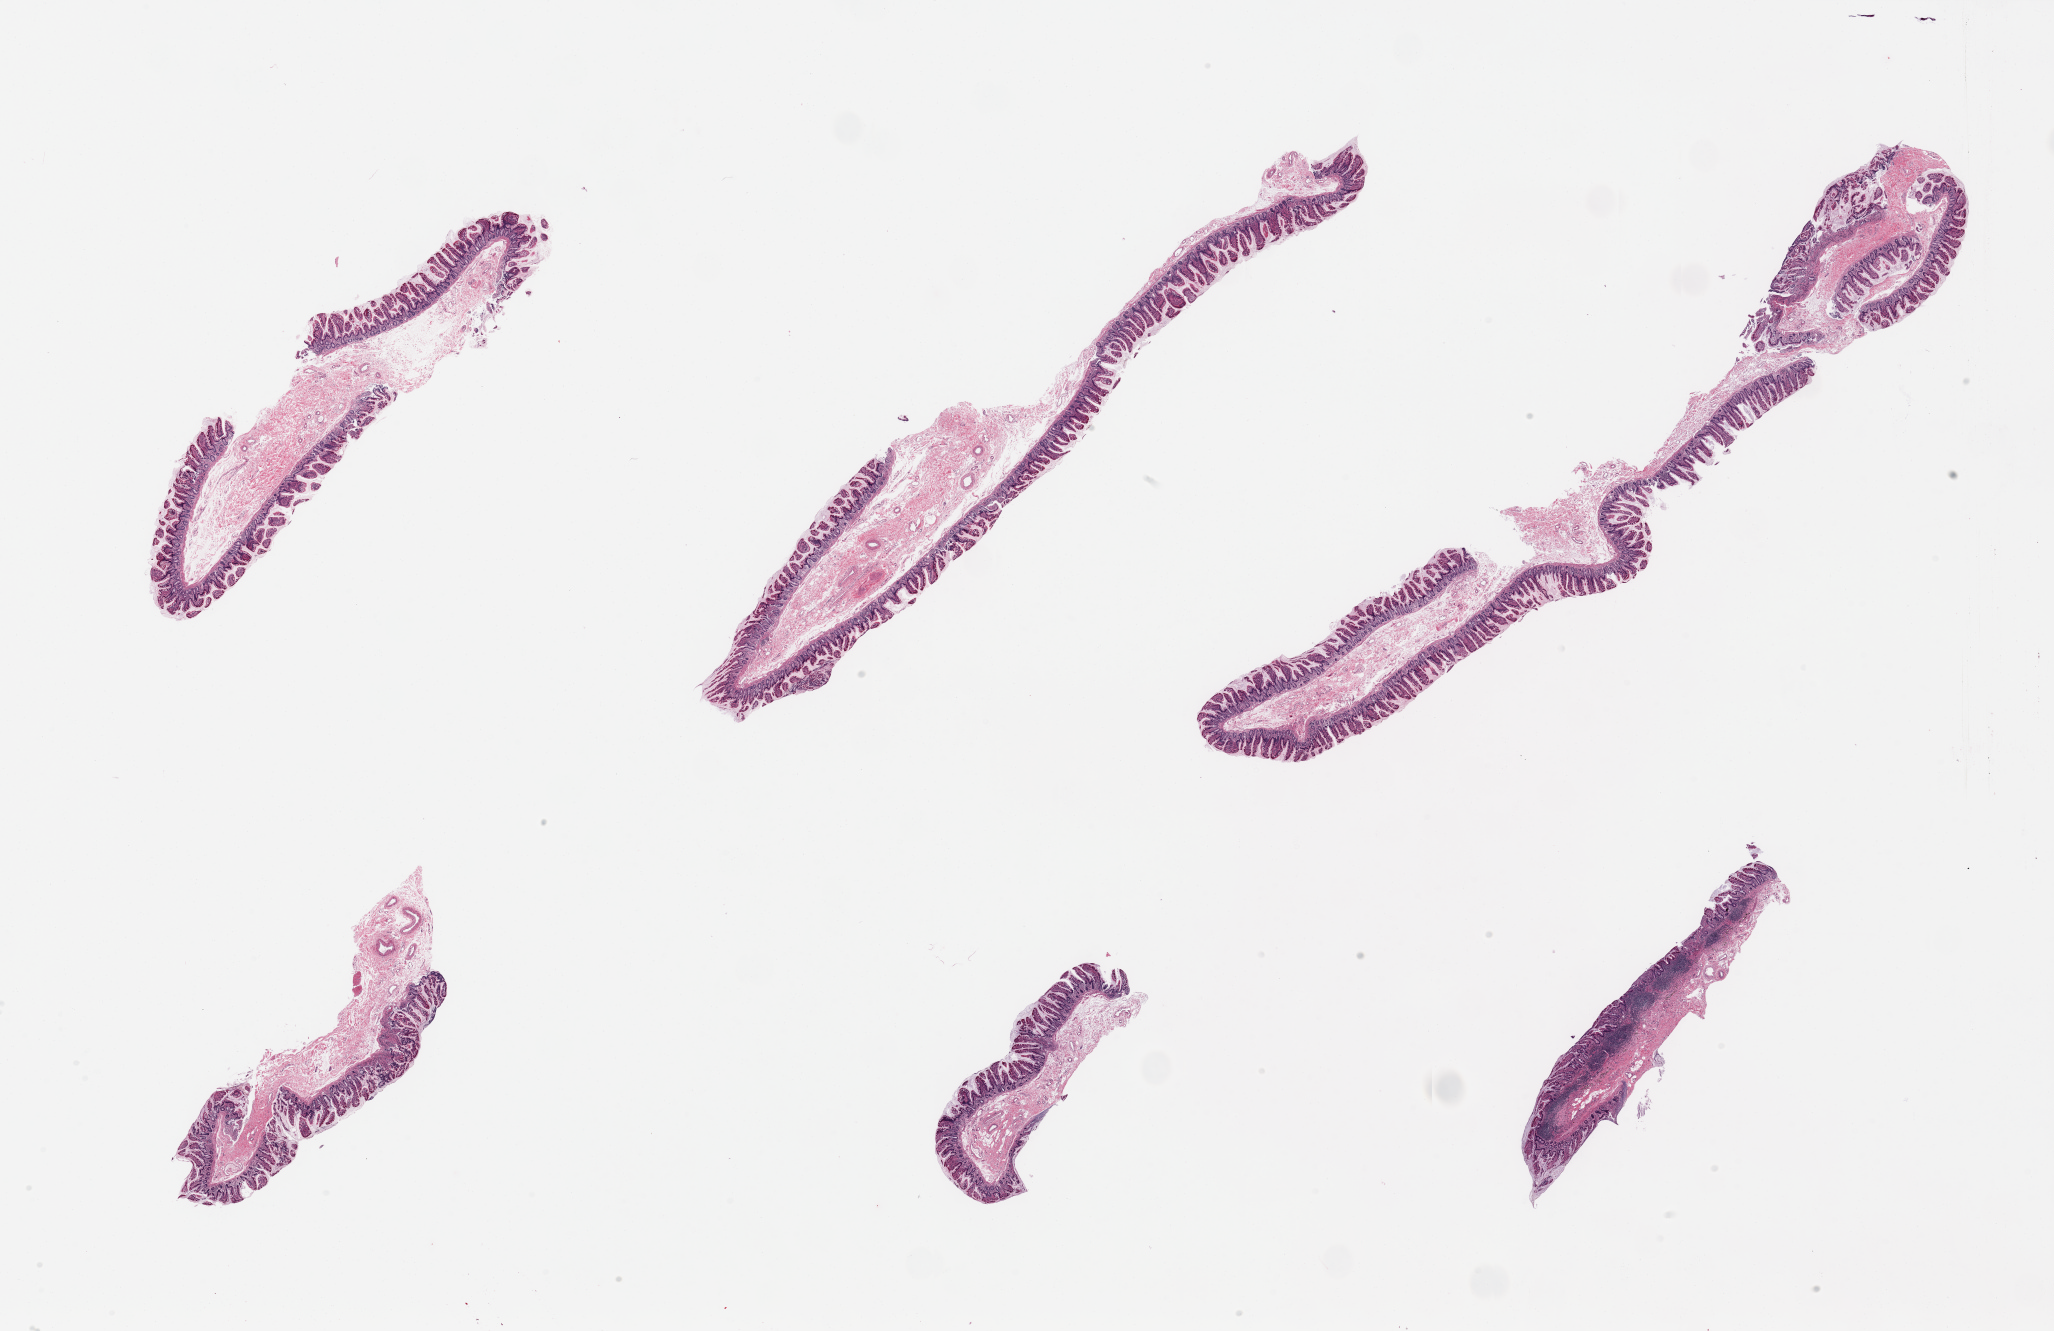
Digitized hematoxylin and eosin (H&E)-stained section, shown as a low-resolution overview of the whole scanned area (about 32.5 x 21.1 mm); PAXgene-fixed, paraffin-embedded tissue; section of ileum (target tissue); tissue donor sample.
Pathologist's review note for this sample: 6 pieces; mucosa and submucosa with only focal lymphoid tissue (1 of 6 pieces).